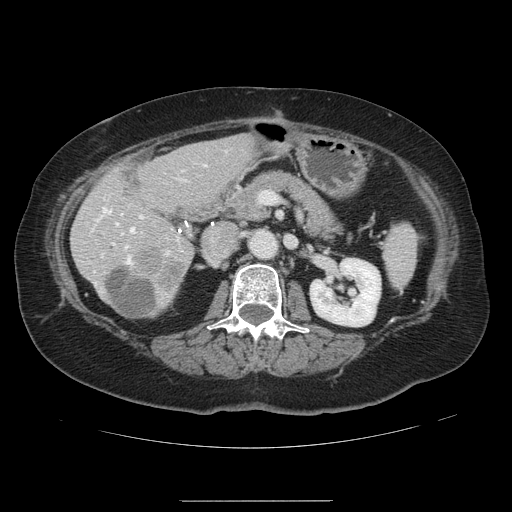
Contrast-enhanced abdominal CT, one axial slice; slice 57 of 141 in the series (ordered by position); soft-tissue window (W 400 / L 40 HU); 2.5 mm slice thickness; 512 × 512 image matrix. Female patient, age 74 years. From the clinical record (not read from this slice): diagnosis: colorectal cancer liver metastases, imaged before liver resection; multiple liver metastases: yes; largest metastasis: 7 cm; disease in both lobes: yes.
Structures marked on this image (manually delineated by an expert):
- hepatic veins: bounding box [x1, y1, x2, y2] px = [97, 208, 134, 264]
- liver: [72, 137, 257, 319]
- planned liver remnant (the part of the liver to remain after resection): [73, 137, 257, 319]
- portal vein (with intrahepatic branches): [113, 164, 238, 254]
- liver metastasis: [109, 269, 161, 316]
- liver metastasis: [138, 247, 187, 291]